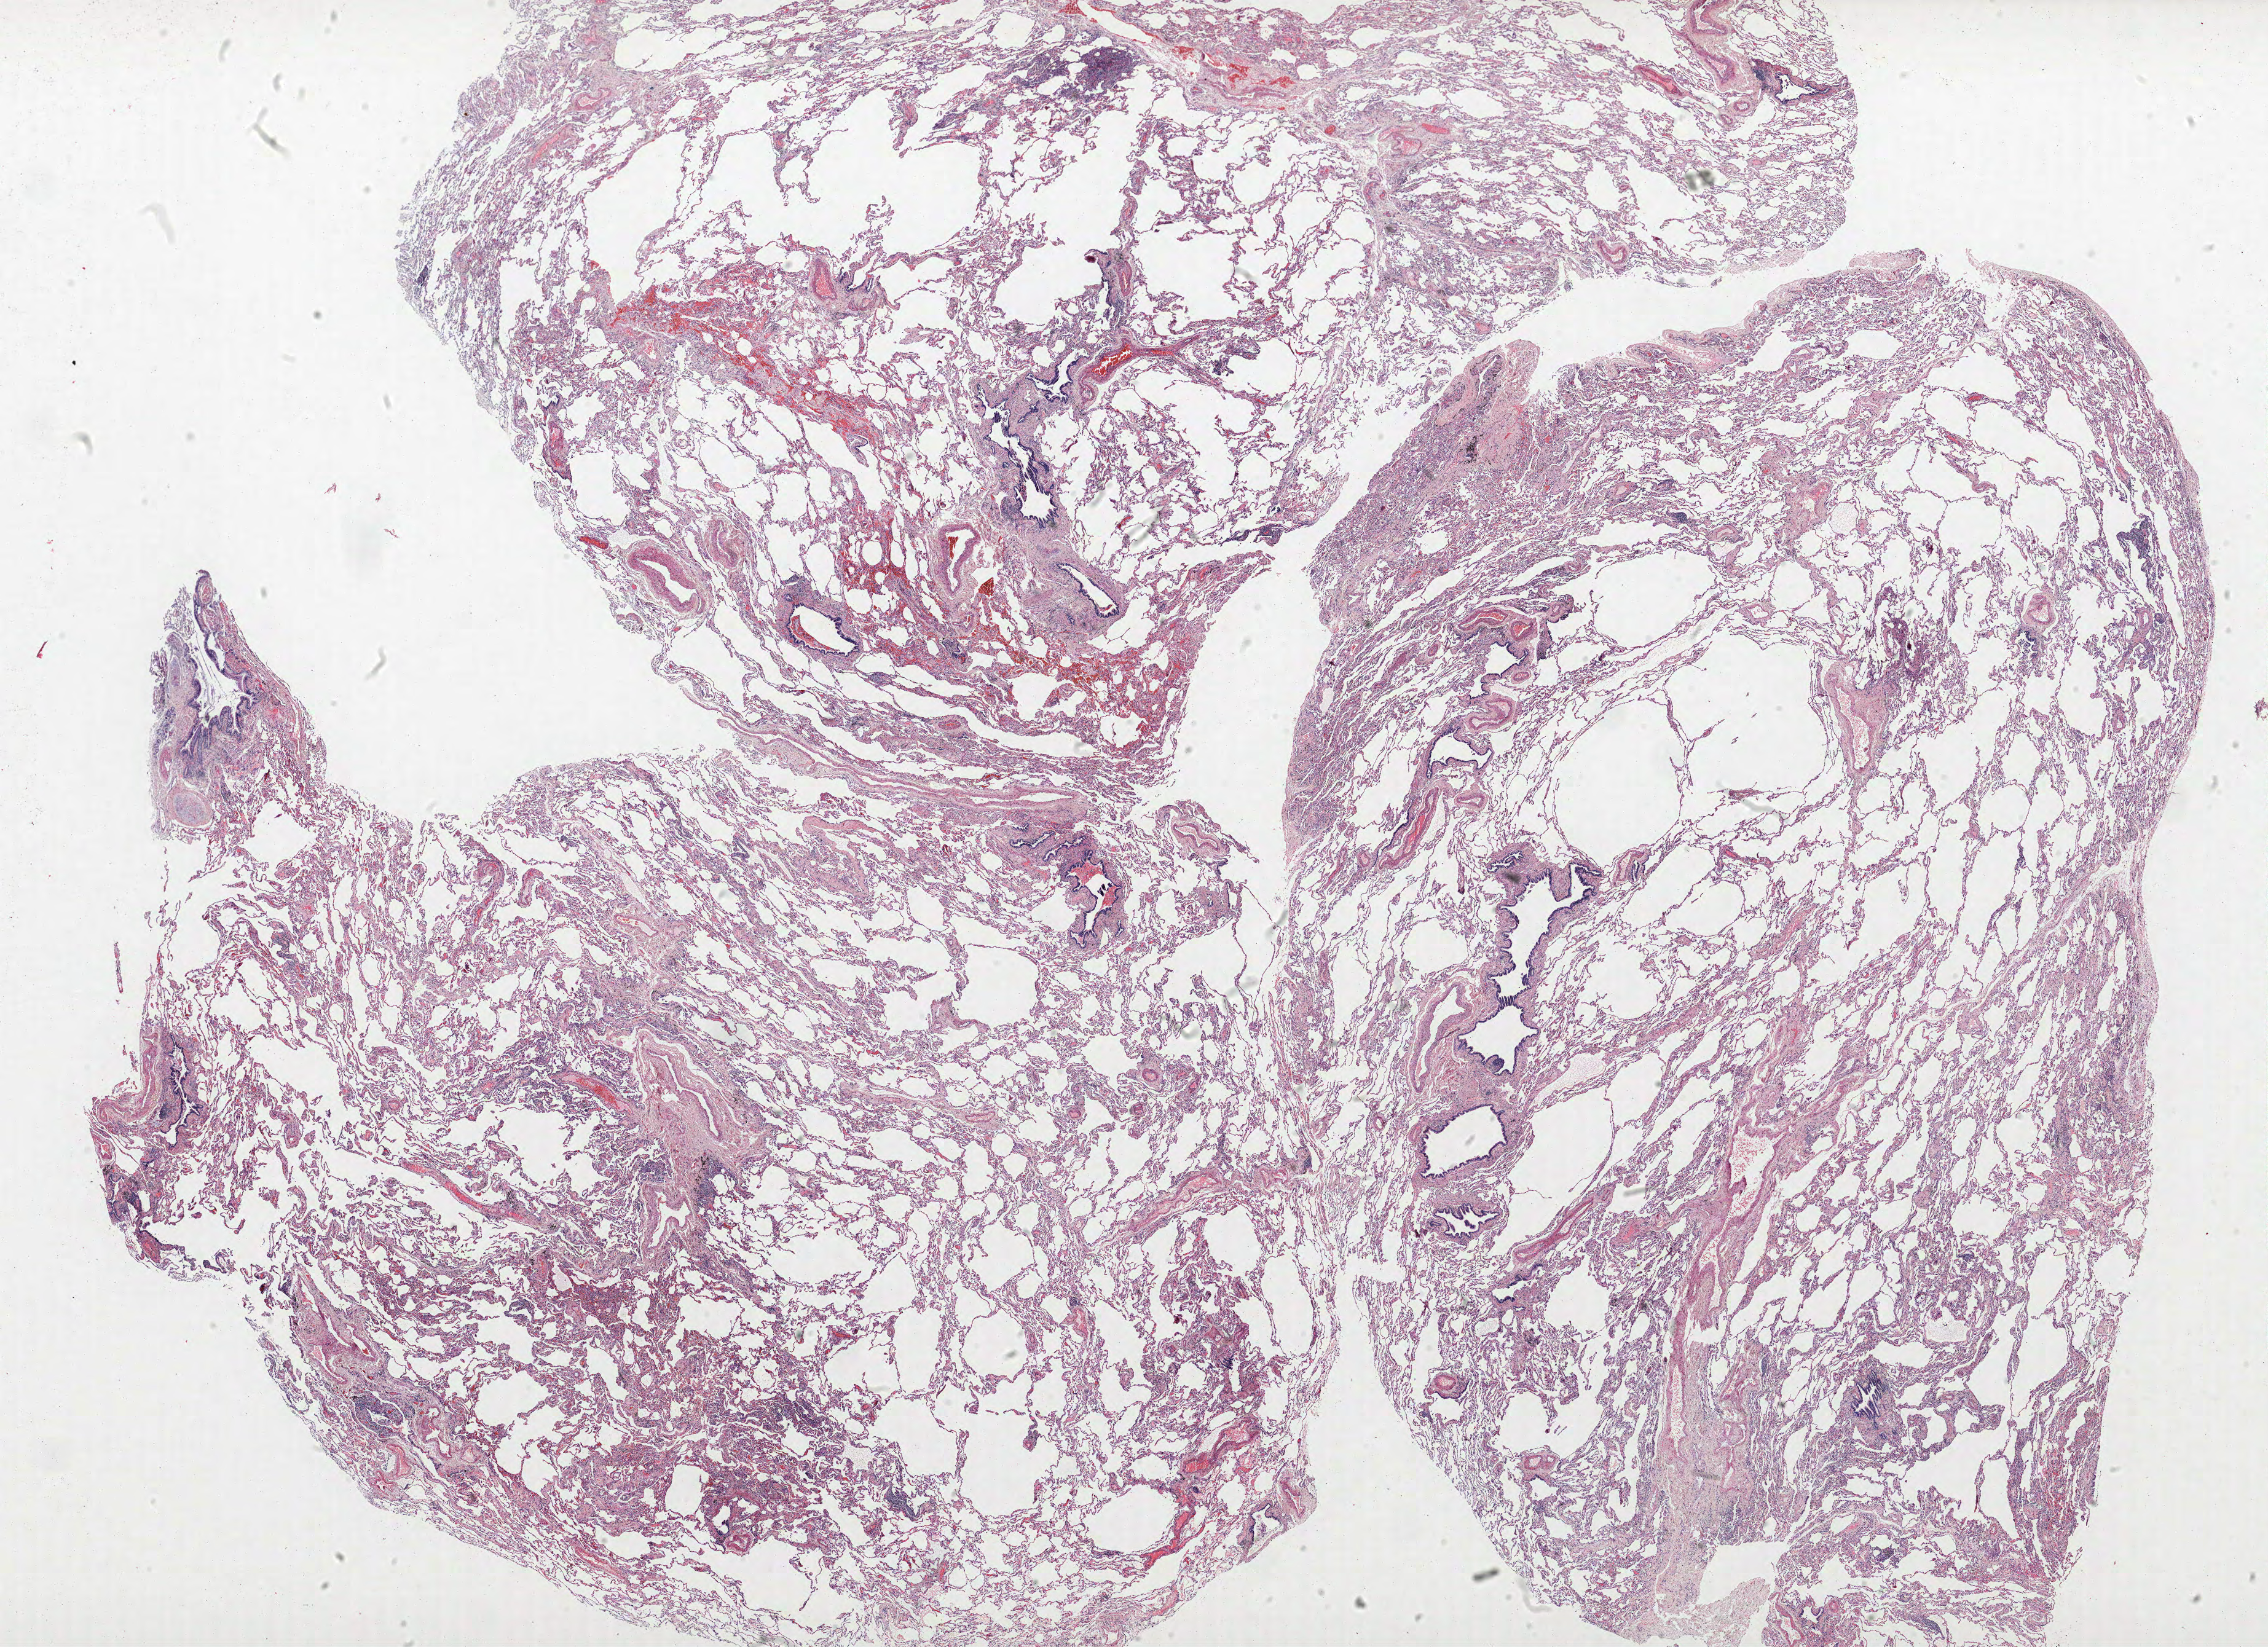
Whole-slide histology image, H&E, low-resolution overview of the scanned area, about 29.5 x 21.4 mm (acquisition: 40x scan); formalin-fixed paraffin-embedded (FFPE) section; lung tissue. Male patient, aged 63 at enrolment. Former smoker at enrolment.
Participant's lung-cancer diagnosis: Squamous cell carcinoma, NOS (ICD-O-3 8070/3).